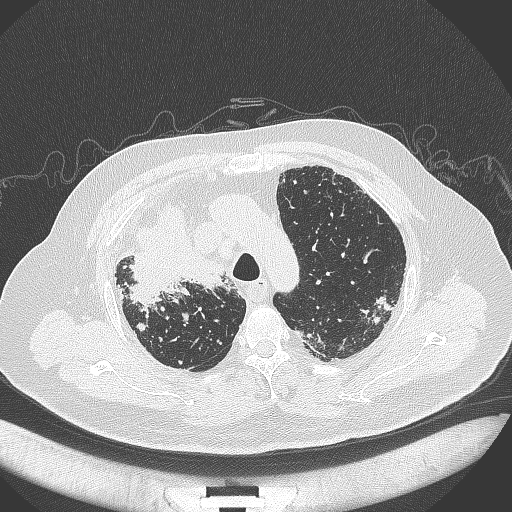
Chest CT, one axial slice; slice 273 of 384 in the series (ordered by position); lung window (W 1500 / L -600 HU); 1 mm slice thickness; 512 × 512 image matrix, field of view 400 × 400 mm. Male patient, age 69 years. From the clinical record (not read from this slice): clinical TNM (as recorded): T4 N3 M1.
Outlined on this slice (bounding box drawn by a radiologist):
- lung tumour (recorded histology: adenocarcinoma): bounding box <125,206,232,314> (left, top, right, bottom; pixels)